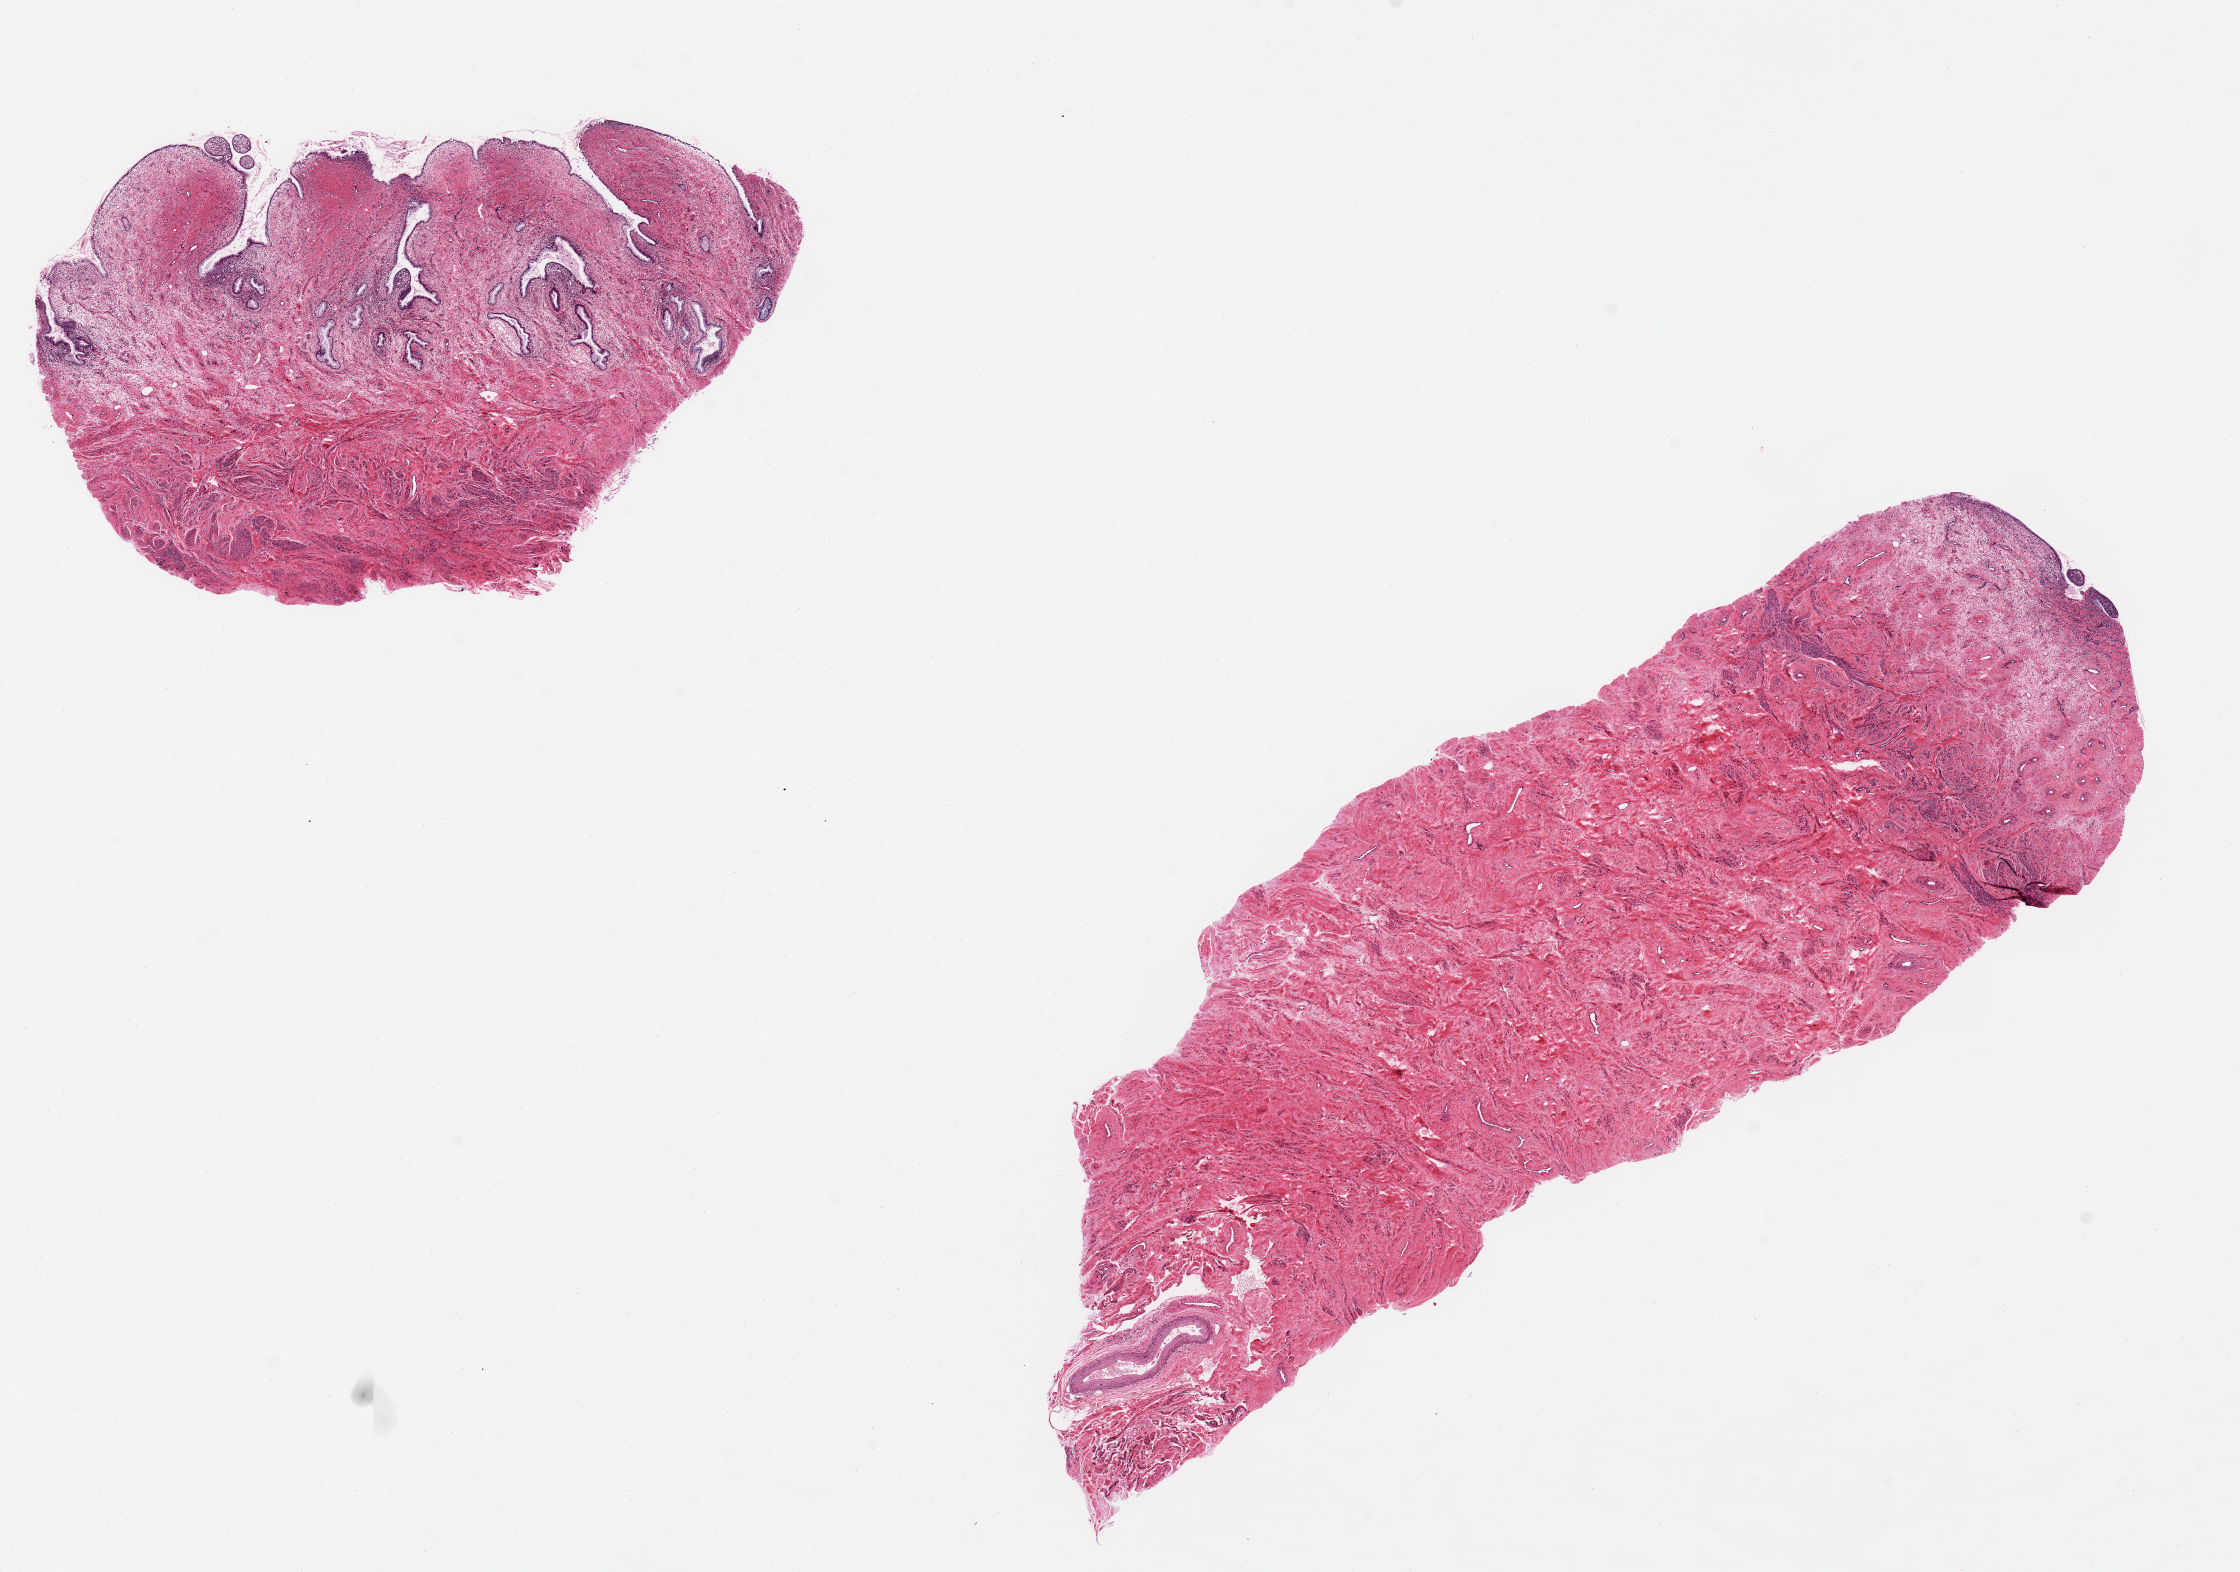
Hematoxylin and eosin (H&E) whole-slide image, shown as a low-resolution overview of the whole scanned area (about 17.7 x 12.4 mm). PAXgene-fixed, paraffin-embedded tissue. Sampled site (target tissue): endocervix. Donor tissue sample. Donor: female.
Reviewer comment on this tissue sample: chronic inflammation, polypoid.